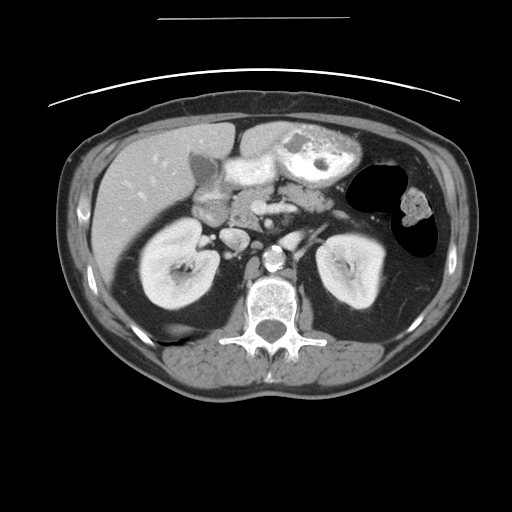
Contrast-enhanced abdominal CT, one axial slice. Position 22 of 49 along the scan axis. Intravenous contrast given. Soft-tissue window (W 400 / L 40 HU). 5 mm slice thickness. 512 × 512 image matrix, field of view 413 × 413 mm. Male patient, age 57 years. From the clinical record (not read from this slice): diagnosis: colorectal cancer liver metastases, imaged before liver resection; multiple liver metastases: yes; largest metastasis: 4 cm; chemotherapy before resection: no.
Annotated regions visible in this slice (manually delineated by an expert):
- hepatic veins: box from (x=150, y=139) to (x=201, y=180) px
- liver: (x=91, y=122)–(x=293, y=283)
- planned liver remnant (the part of the liver to remain after resection): (x=213, y=122)–(x=293, y=159)
- portal vein (with intrahepatic branches): (x=138, y=160)–(x=167, y=197)